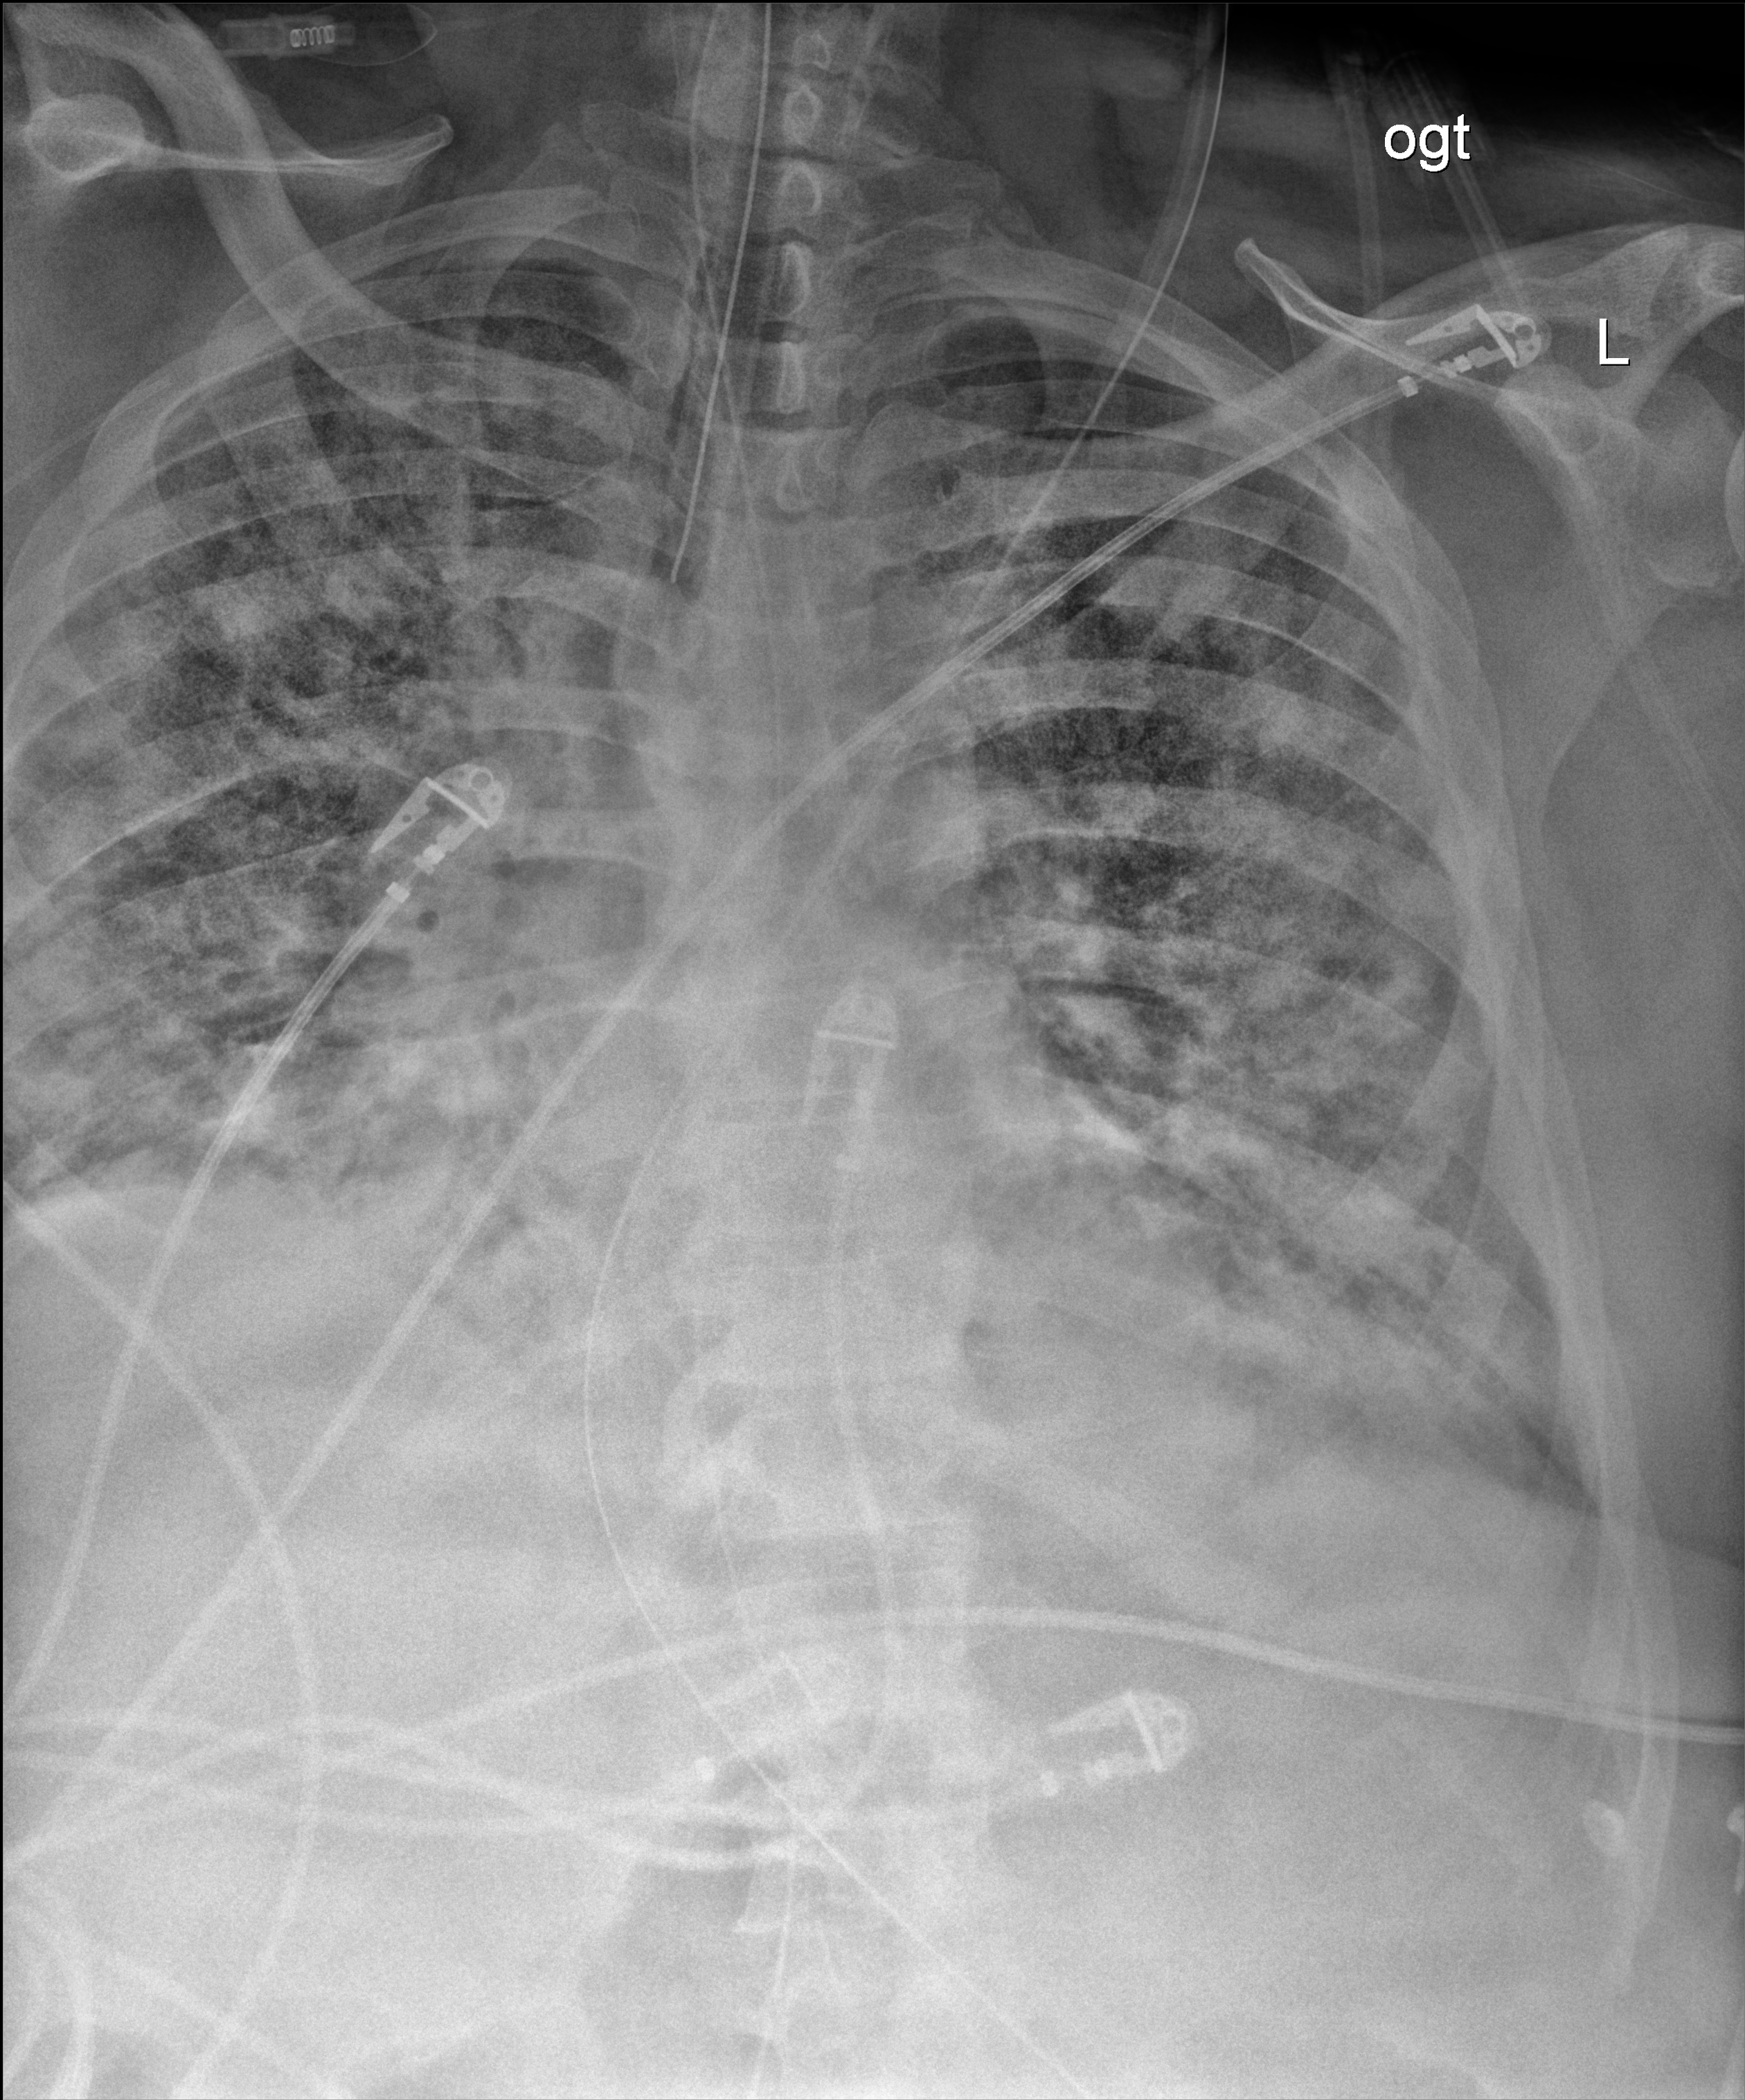
Chest X-ray (portable); anteroposterior (AP) projection. Male patient hospitalised with COVID-19, age 60–74 years.
From the hospital-stay record, not from the radiograph (when in the stay this image was taken is not recorded):
- mechanically ventilated during this hospital stay: yes
- length of hospital stay: 34 days